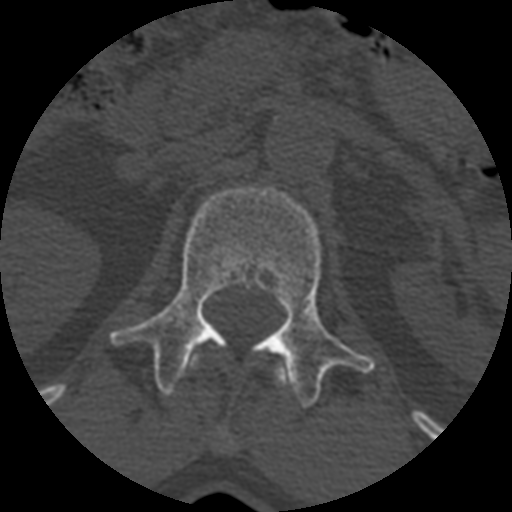
CT including the spine, one axial slice. Slice 364 of 399 in the series (ordered by position). Reconstruction kernel STANDARD. Bone window (W 1800 / L 400 HU). 1.25 mm slice thickness. 512 × 512 image matrix, field of view 160 × 160 mm. Patient age 71 years. From the clinical record (not read from this slice): primary cancer: prostate.
Annotated regions visible in this slice (semi-automatically segmented with operator editing):
- L1 vertebra: bounding box (x1, y1, x2, y2) in pixels: (111, 180, 374, 407)
- T12 vertebra: (190, 359, 283, 388)